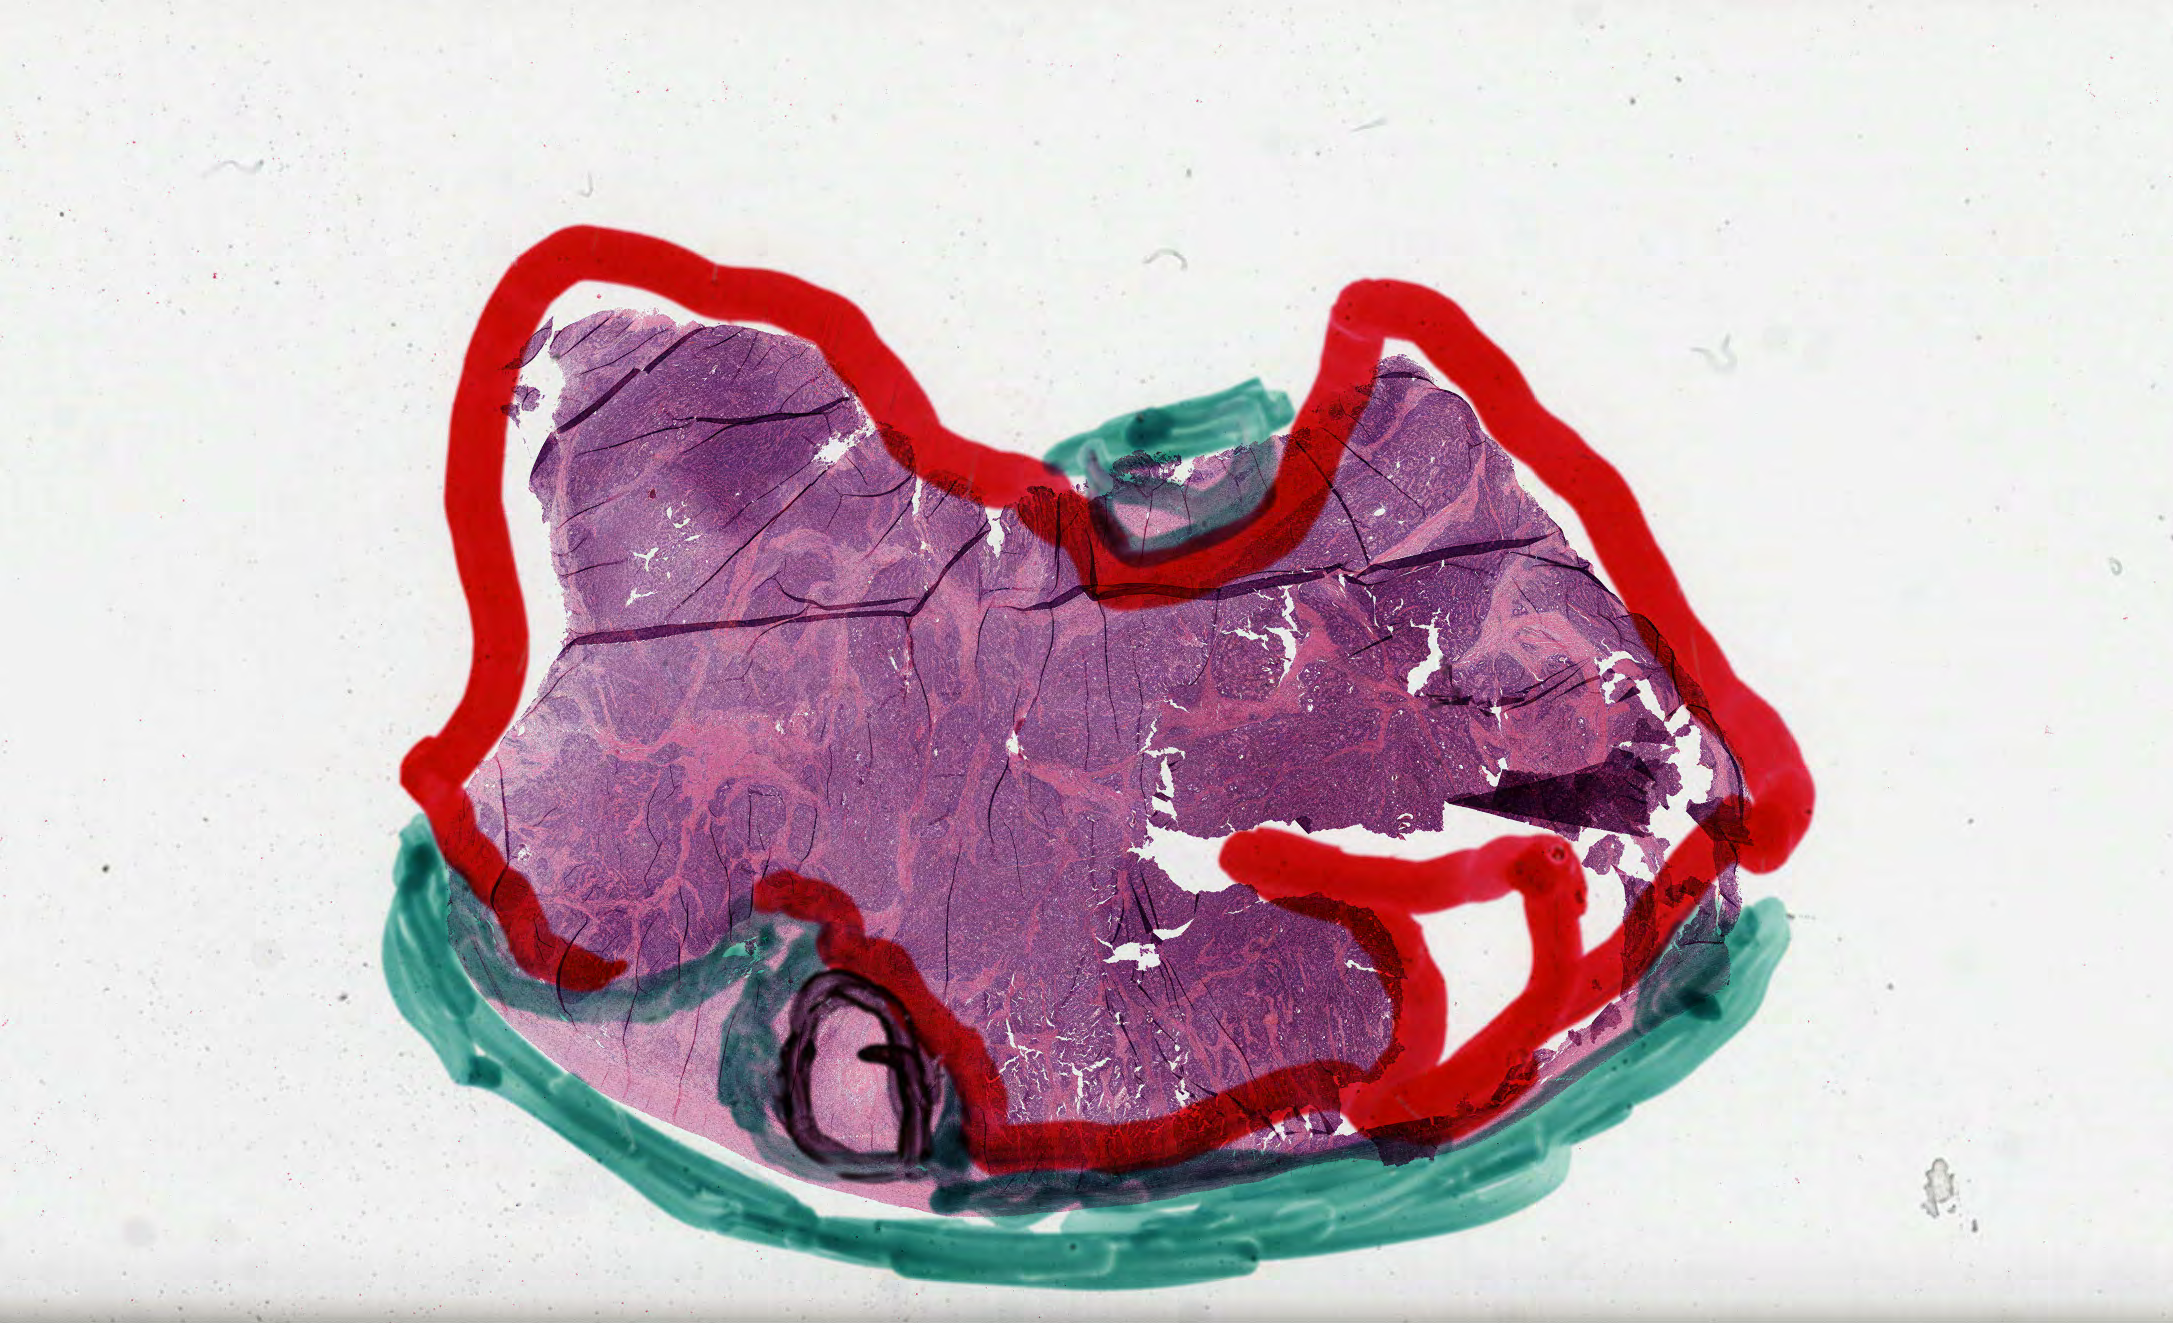
Hematoxylin and eosin (H&E) stained whole-slide image, low-resolution overview of the scanned area, about 35.1 x 21.3 mm; formalin-fixed paraffin-embedded (FFPE) diagnostic section; sample: primary tumour, stomach. Male, age 75 years at initial diagnosis. Histologic grade: G3 (poorly differentiated).
* AJCC pathologic stage: IIA (7th edition)
* lymph nodes positive (case pathology): 0 of 15 examined
* diagnosis: Adenocarcinoma, NOS (body of stomach)